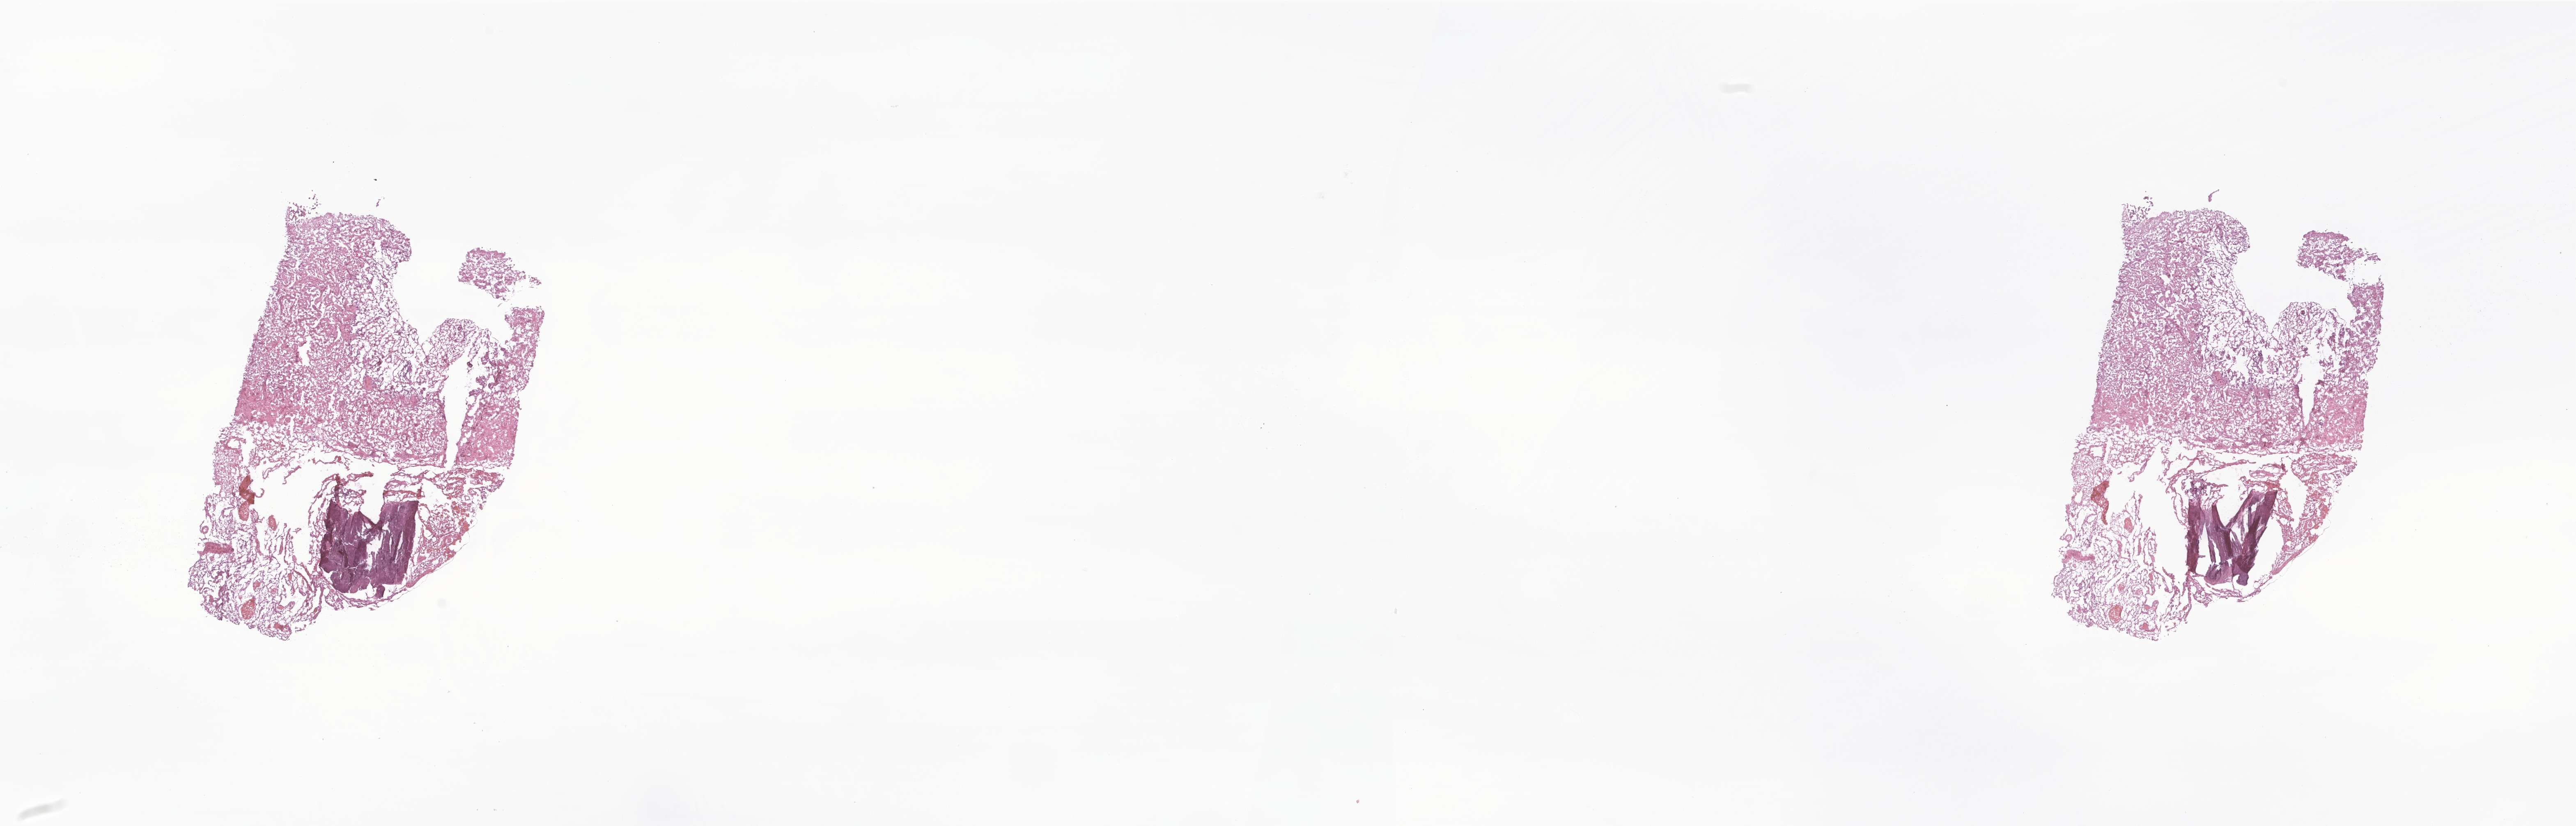
Whole-slide image, haematoxylin and eosin stain of tumor tissue from the brain — whole scanned area (about 26.5 x 8.5 mm) shown as a low-resolution overview. Frozen section (OCT-embedded). Female patient, age 200 months (16 years 8 months).
Diagnosis (ICD-O-3 morphology term): Meningioma, NOS.